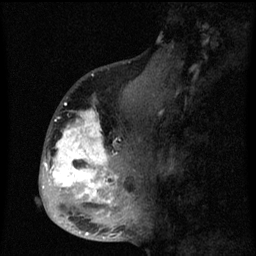
Breast MRI (dynamic contrast-enhanced), one sagittal slice. Position 28 of 60 along the scan axis. Dynamic contrast-enhanced series, image 2 of 3 at this slice position (ordered by acquisition). 1.5 T. TE 4.2 ms, TR 8 ms. 2 mm slice thickness. 256 × 256 image matrix, field of view 190 × 190 mm. Patient: female, 50 years.
Annotated regions visible in this slice (semi-automatically segmented with operator editing):
- analysis volume of interest (the breast-tissue region the enhancement analysis was run in; not a lesion): bounding box <43,90,142,216> (left, top, right, bottom; pixels)
- tumour enhancement mask (voxels above the 70 % enhancement threshold inside the analysis volume of interest): <43,110,124,216>